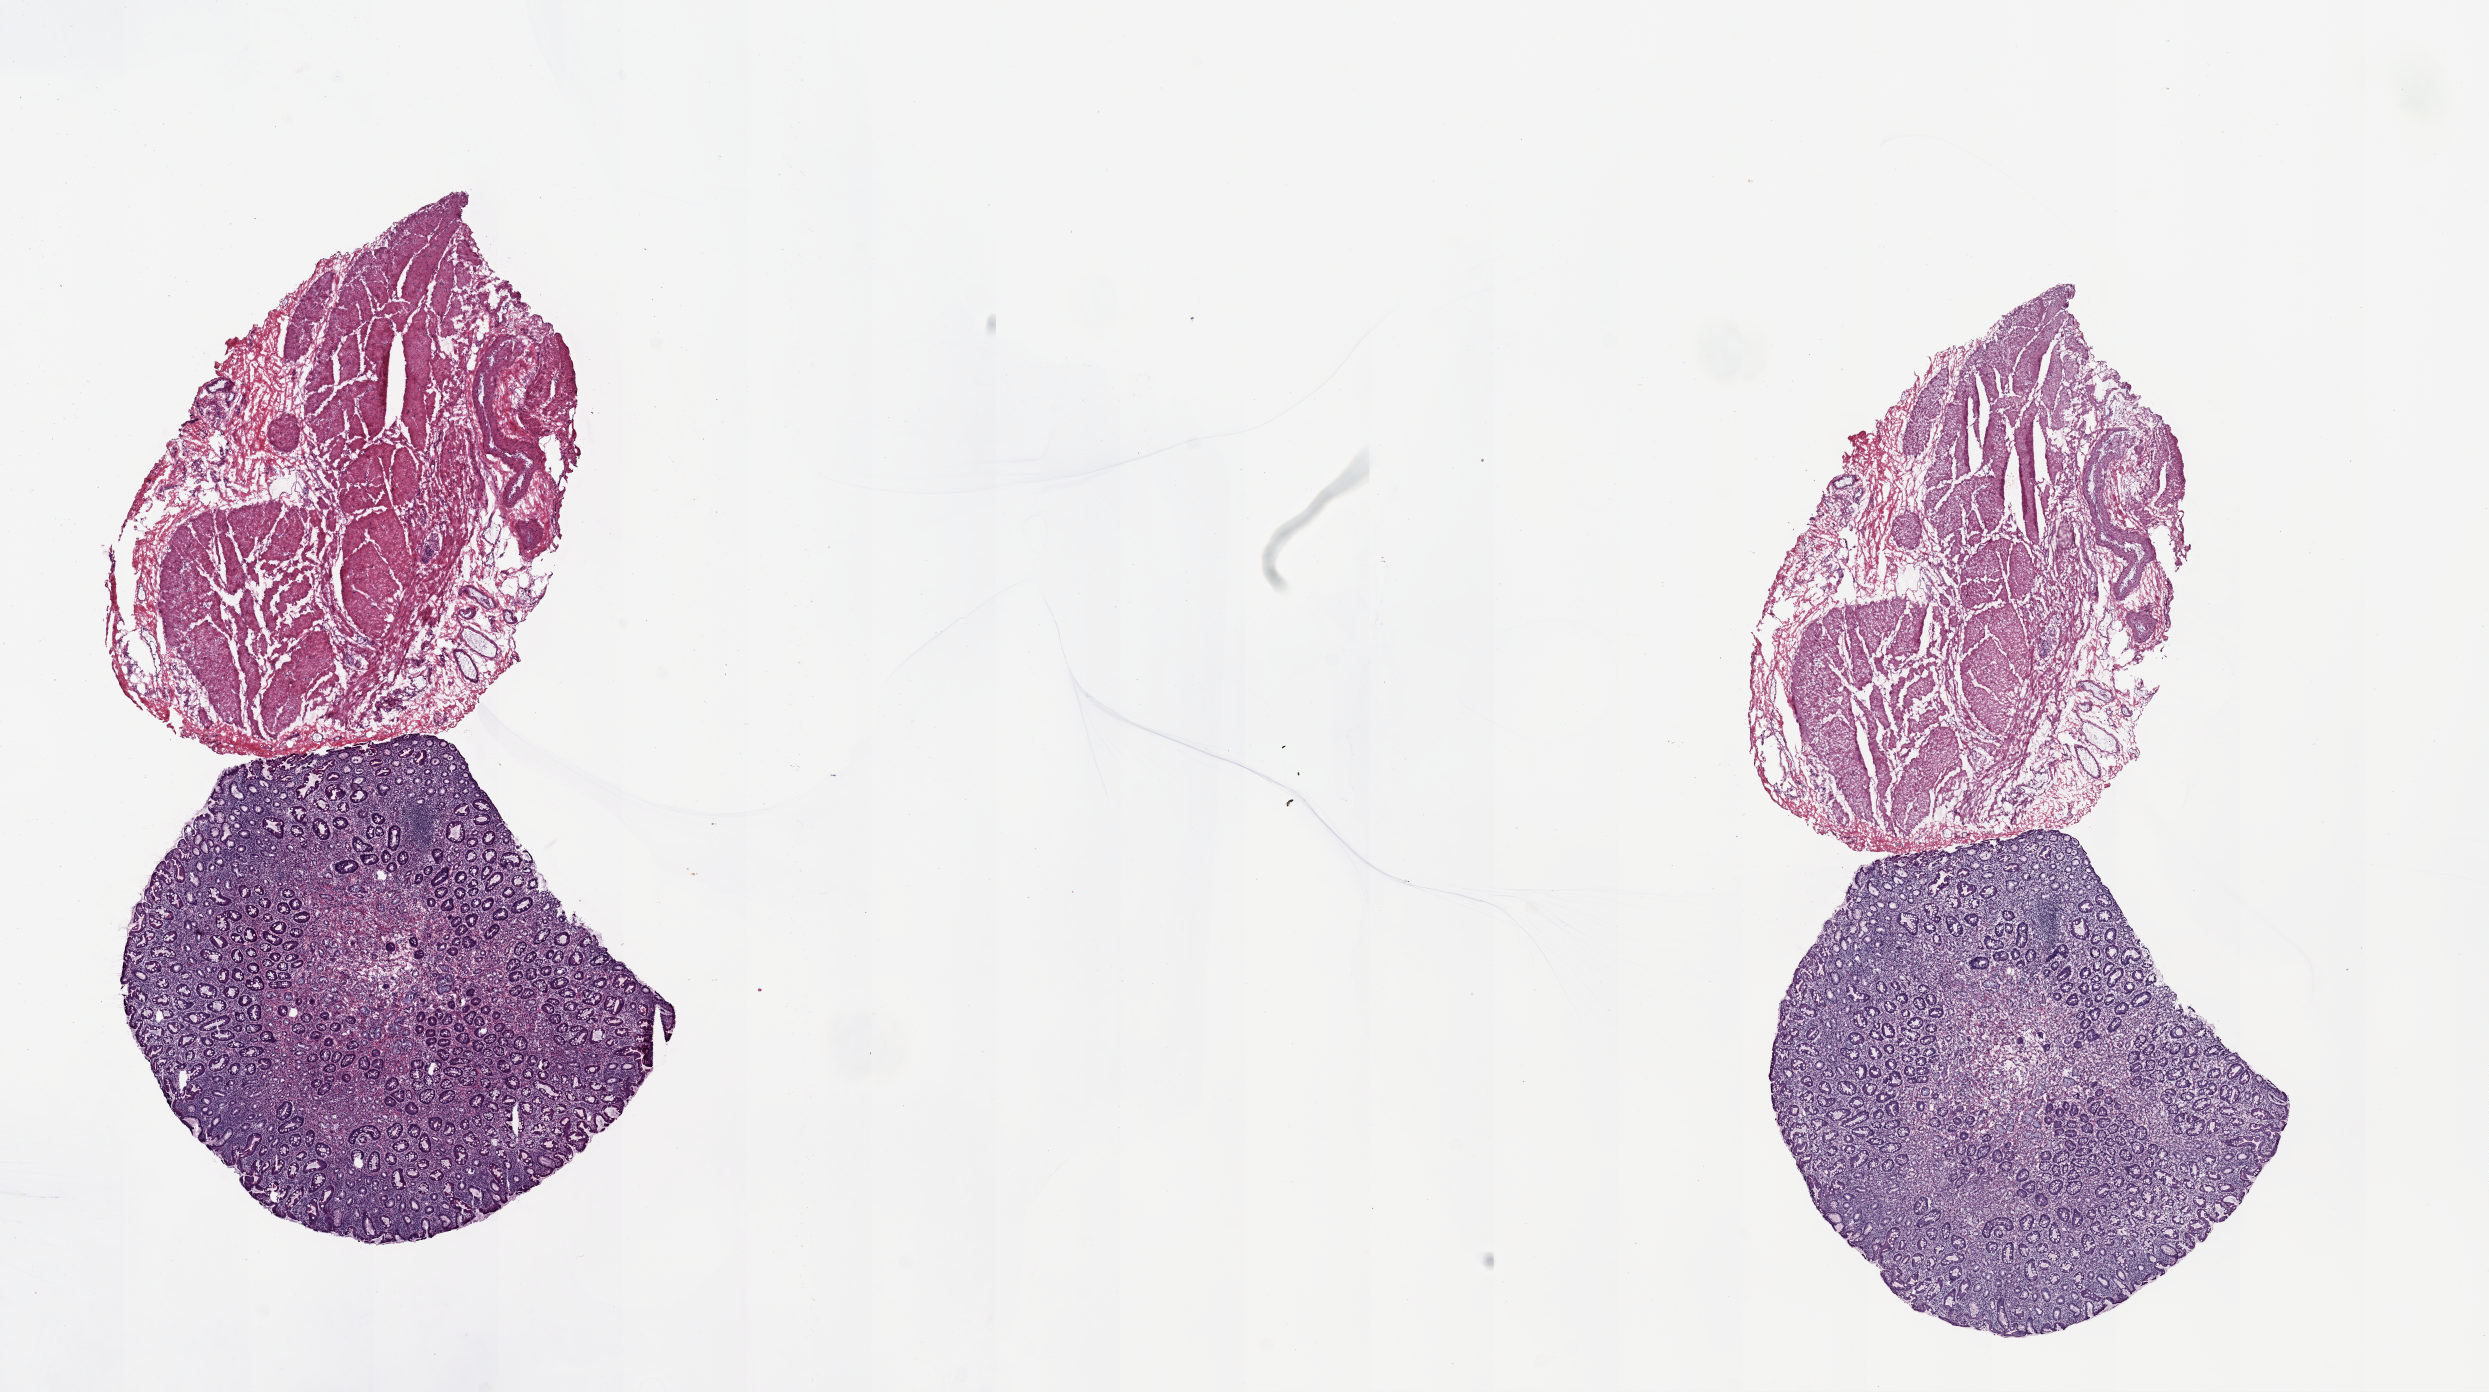
Whole-slide histology image, Hematoxylin and eosin (H&E) stained, shown as a low-resolution overview of the whole scanned area (about 19.6 x 11.0 mm, slide scanned at 20x). Frozen section. Stomach, solid tissue normal (non-tumour tissue) sample. Patient: male, age at initial diagnosis 75 years. Slide review estimates, as recorded: tumour cells 0%, tumour nuclei 0%, normal cells 100%, stromal cells 0%, necrosis 0%. Infiltration values recorded for this section: lymphocyte infiltration 20%, monocyte infiltration 1%, neutrophil infiltration 1%.
This section: solid tissue normal (non-tumour) sample from the same patient. Patient diagnosis: Tubular adenocarcinoma.